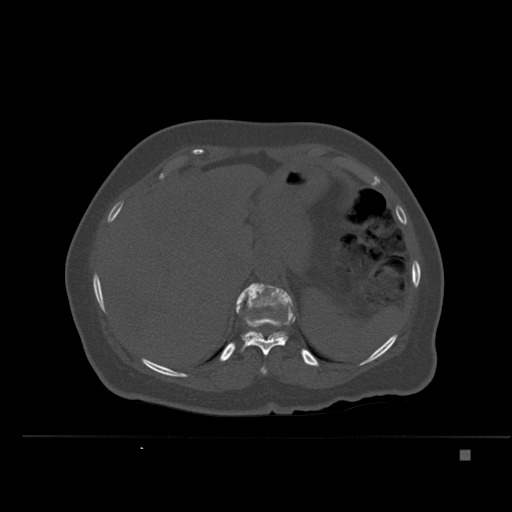
CT including the spine, one axial slice; slice 266 of 477 in the series (ordered by position); bone window (W 1800 / L 400 HU); 1.5 mm slice thickness; 512 × 512 image matrix, field of view 422 × 422 mm. Female patient, age 74 years. Case-level facts recorded for this patient, not image findings: primary cancer: colon.
Annotated regions visible in this slice (semi-automatic segmentation, software-assisted and operator-edited):
- T10 vertebra: bounding box (x1, y1, x2, y2) in pixels: (260, 366, 267, 375)
- T11 vertebra: (240, 311, 295, 356)
- T12 vertebra: (236, 283, 293, 338)